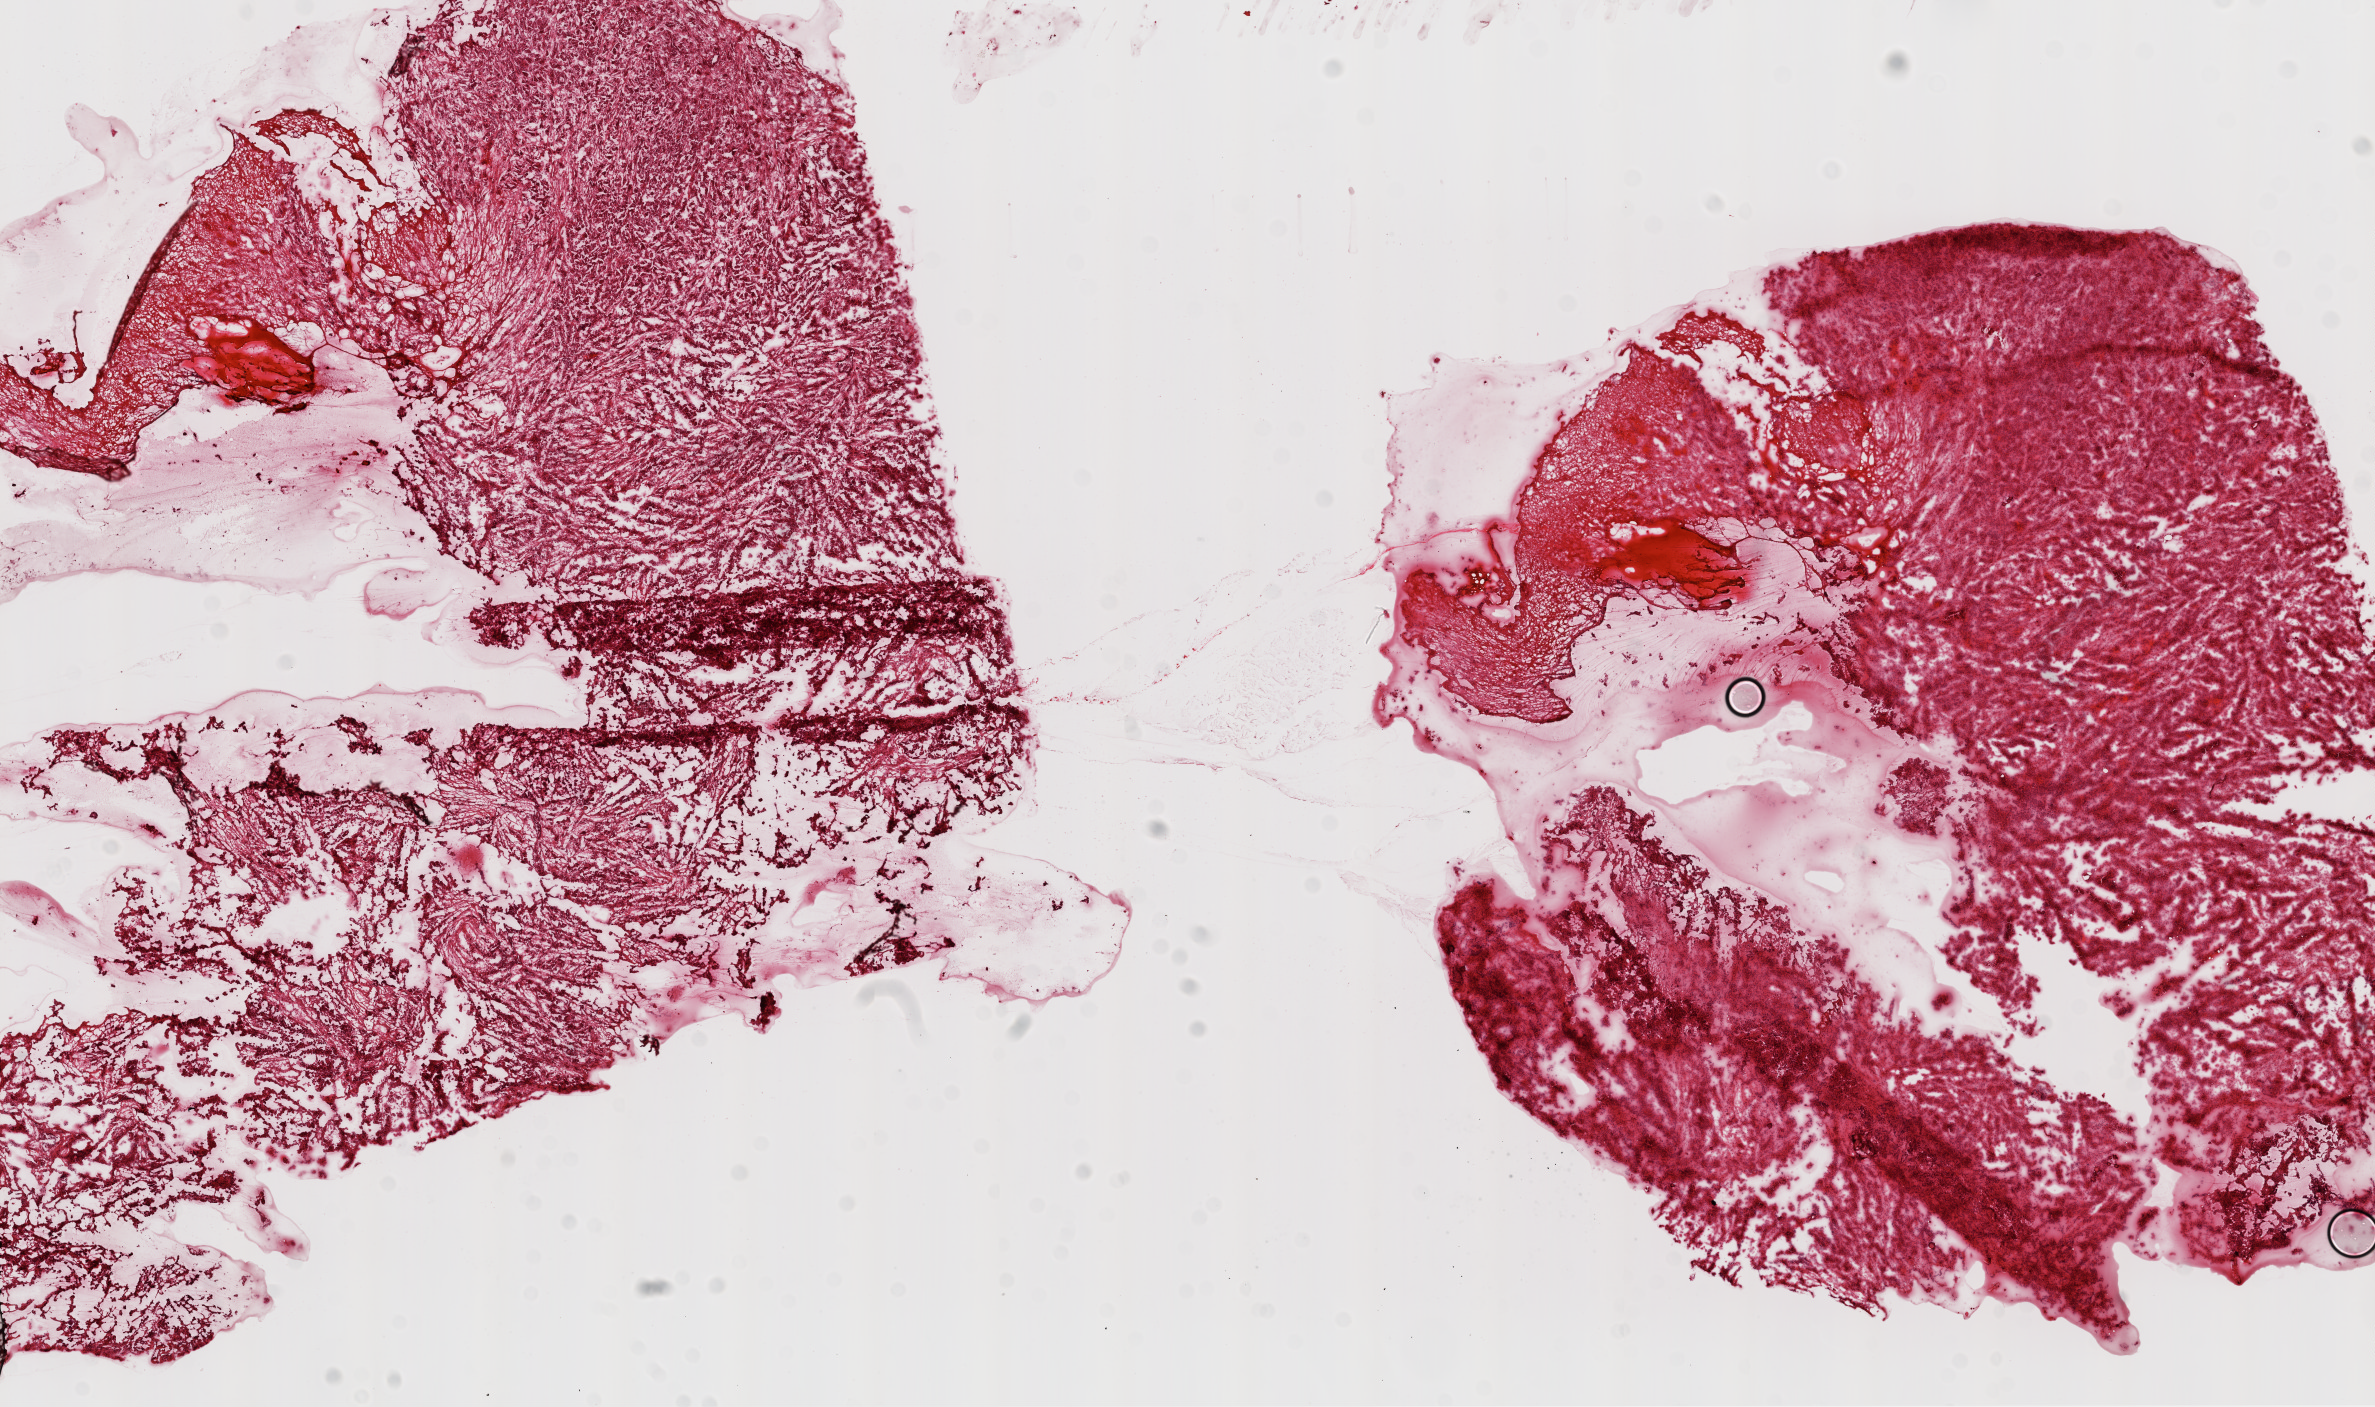
Digitized H&E tissue section (whole slide), a low-resolution overview of the entire scanned area, about 19.1 x 11.3 mm, frozen section from the top of the tissue portion, ovary, primary tumour sample. Female patient; age at initial diagnosis 59 years. Histologic grade: G3 (poorly differentiated). Pathologist review of this section (percent, as recorded): tumour cells 89%, tumour nuclei 90%, normal cells 0%, stromal cells 10%, necrosis 1%.
* FIGO stage: IIIC
* laterality: bilateral
* histologic diagnosis: Serous cystadenocarcinoma, NOS